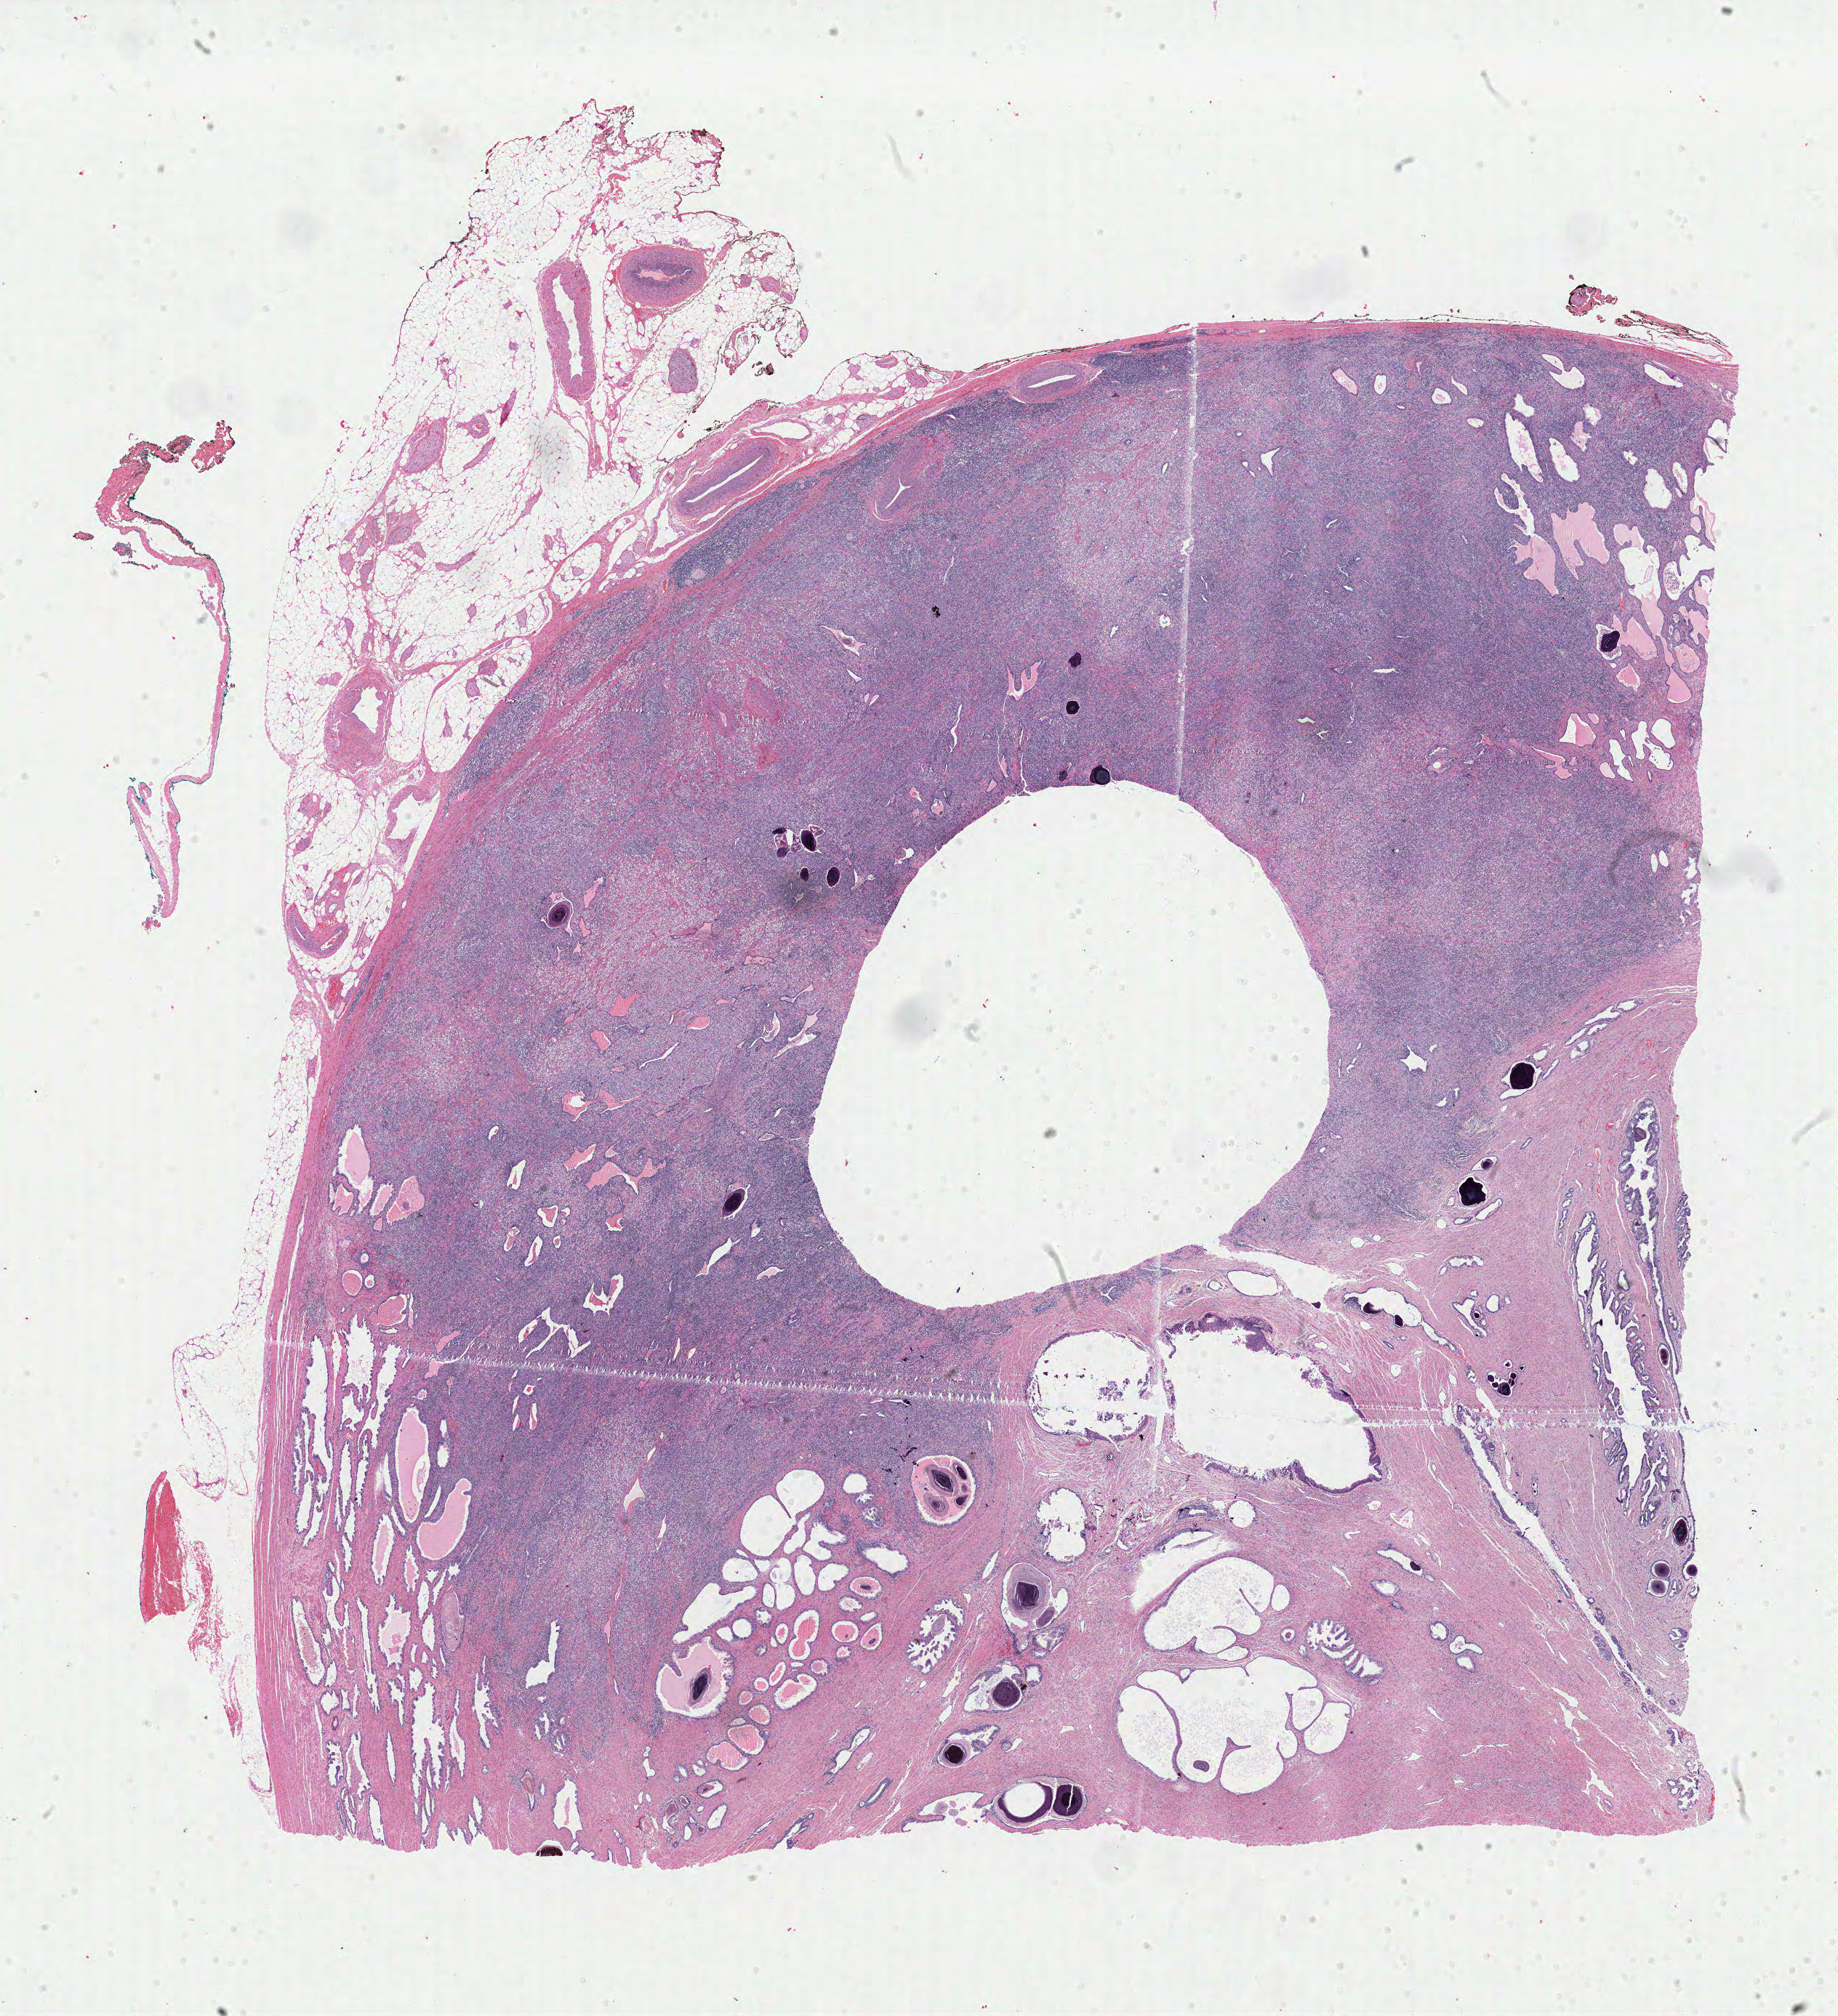
H&E-stained whole-slide image, shown as a low-resolution overview of the whole scanned area (about 20.0 x 21.9 mm, acquisition: 40x scan). Formalin-fixed paraffin-embedded (FFPE) diagnostic section. Prostate, primary tumour sample. Male, age 64 years at initial diagnosis.
Pathologic diagnosis: Adenocarcinoma, NOS (prostate gland).